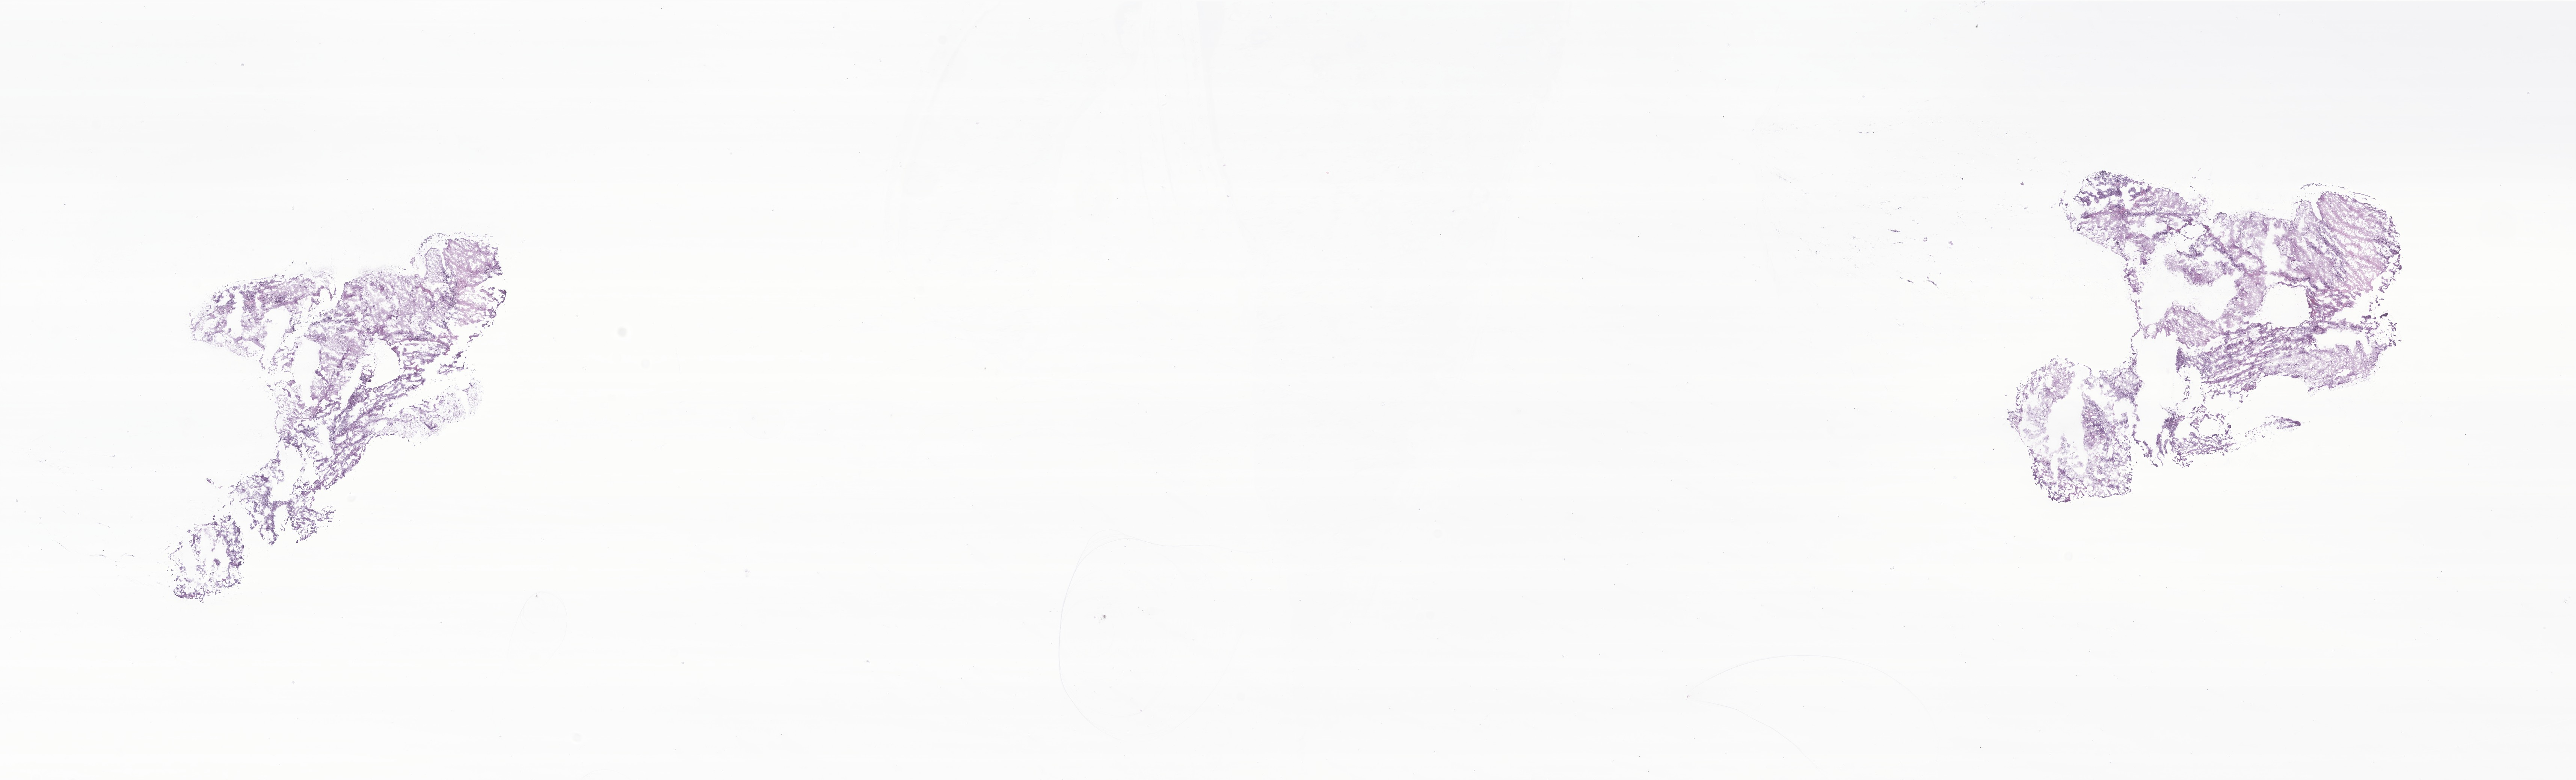
Haematoxylin and eosin whole-slide image of tumor tissue from the brain, shown as a low-resolution overview of the whole scanned area (about 28.9 x 8.8 mm). Frozen section. Female patient, age 45 months.
Diagnosis (ICD-O-3 morphology term): Neoplasm, uncertain whether benign or malignant.